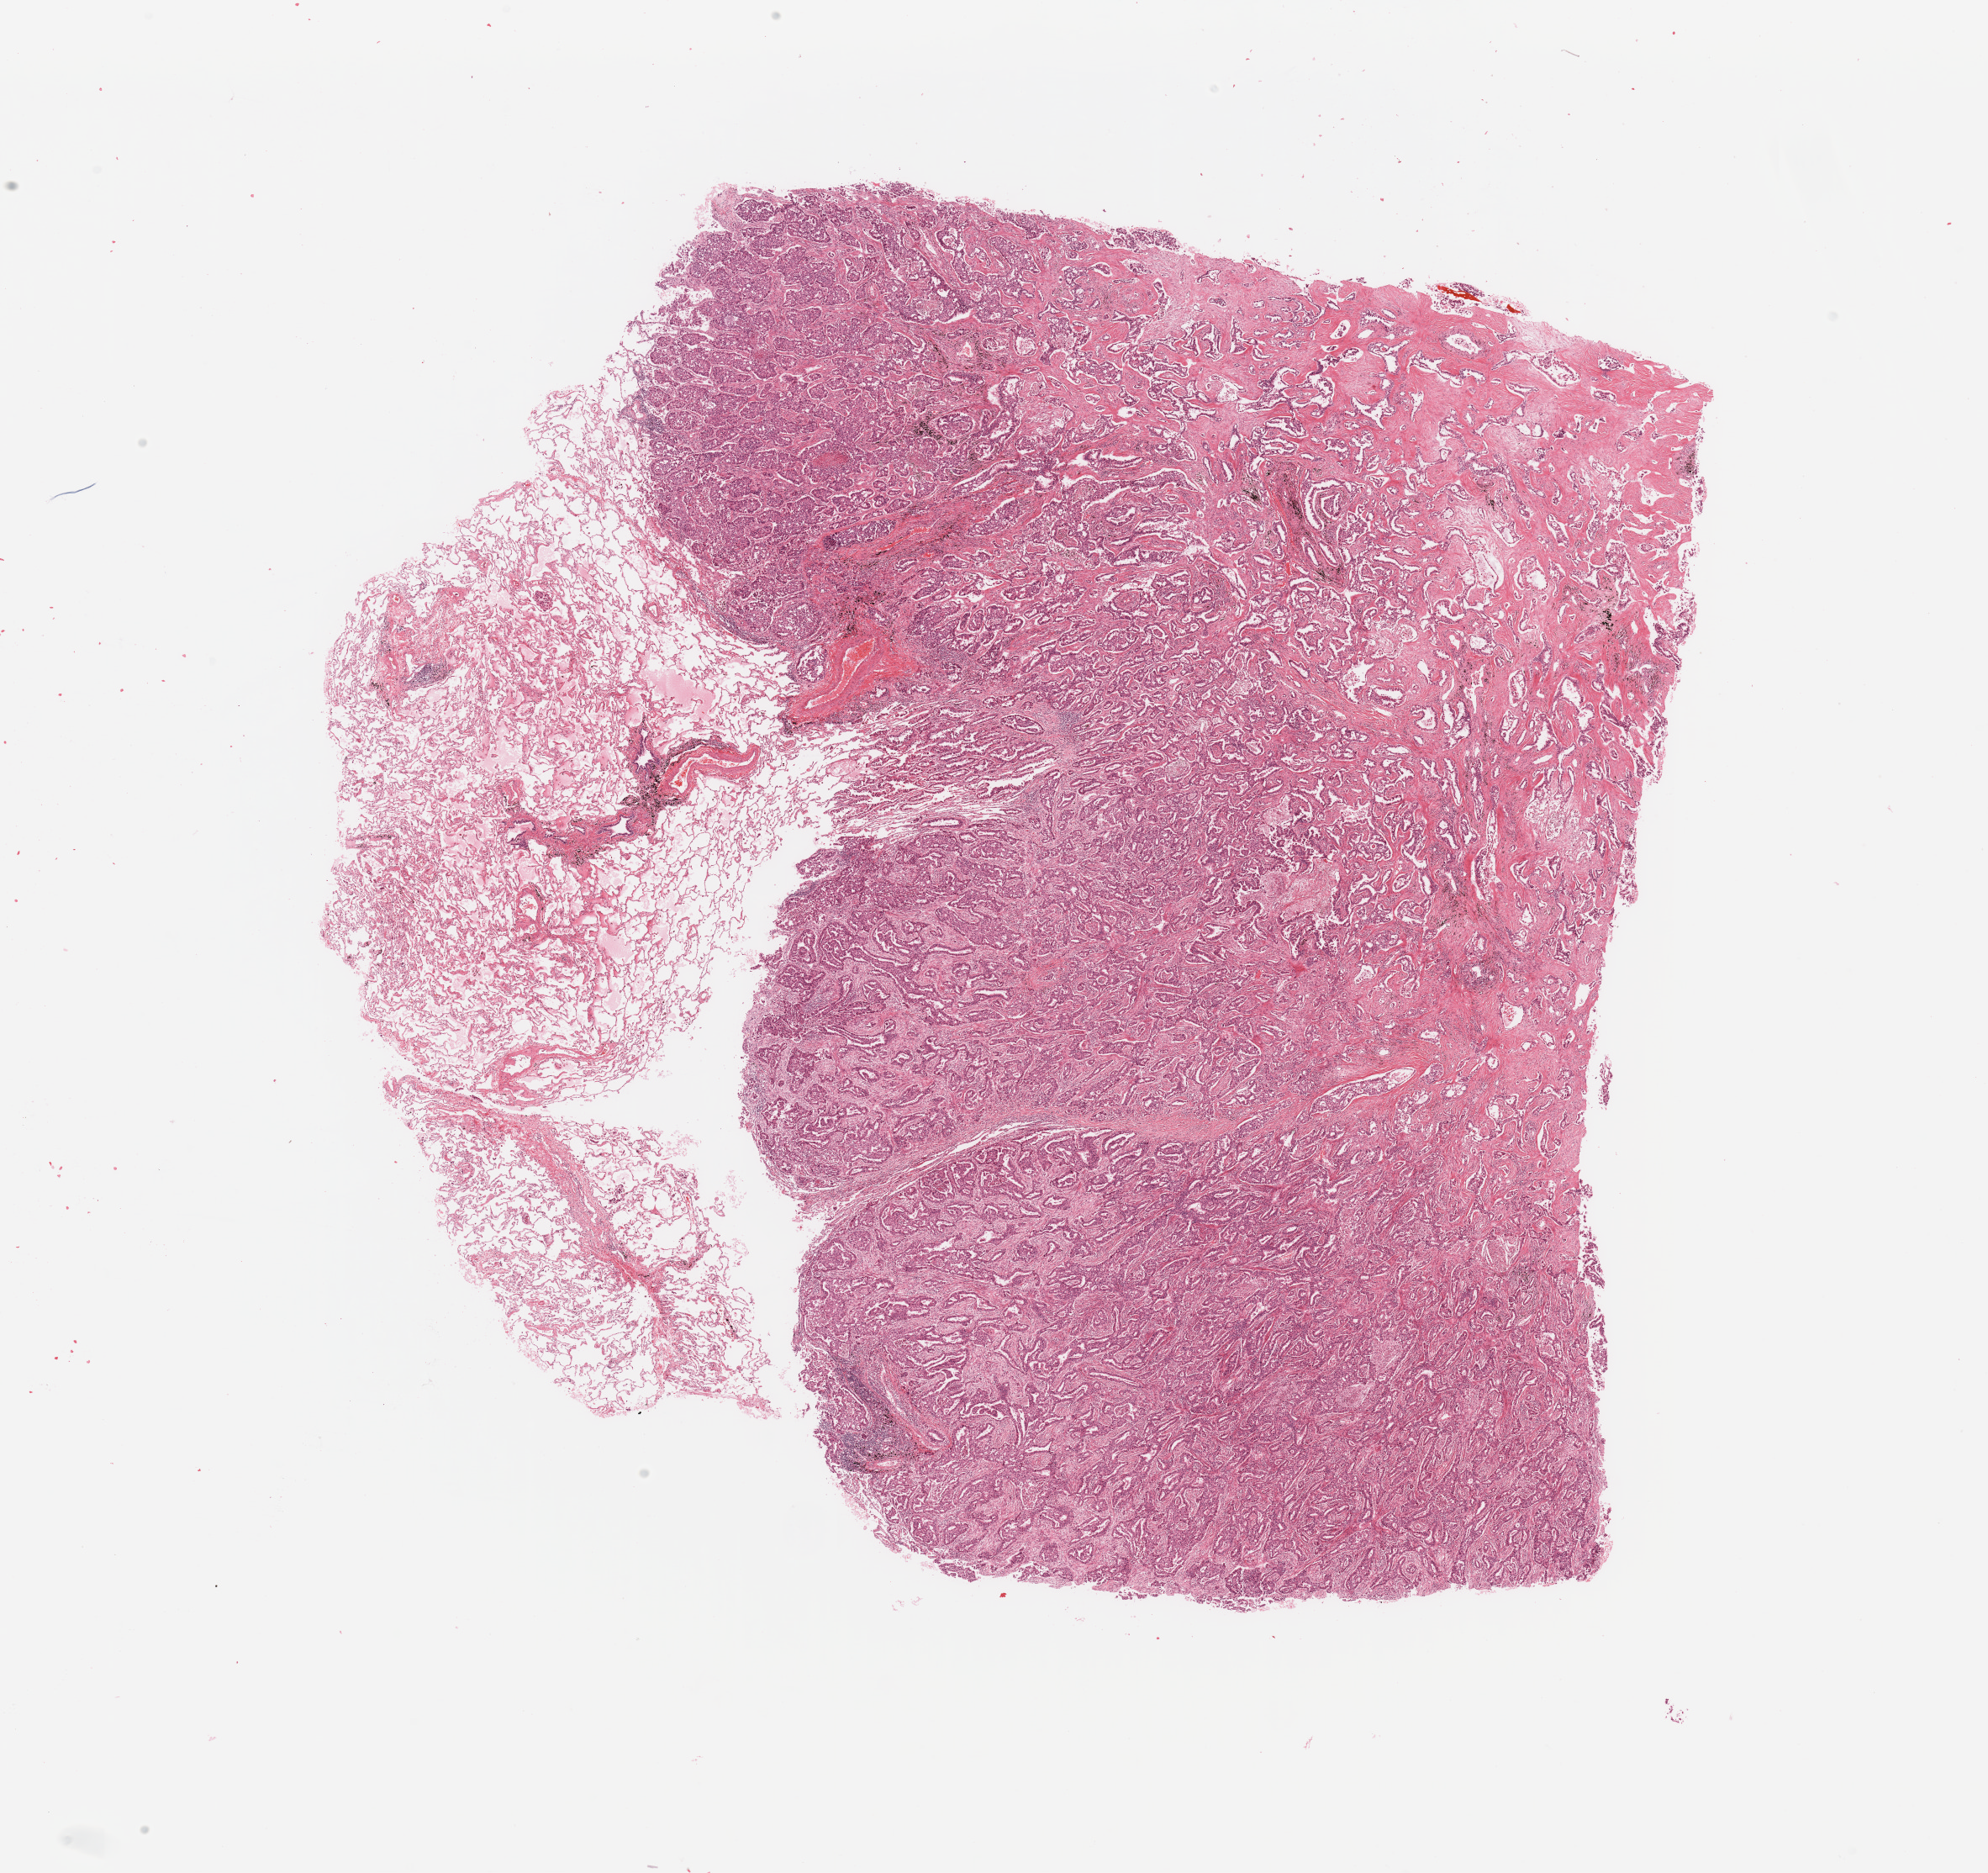
Whole-slide histology image, H&E — shown as a low-resolution overview of the whole scanned area (about 18.7 x 17.6 mm, from a 20x scan), tumour tissue sample, lung. 55-year-old female patient. Histologic grade: G2 (moderately differentiated).
* AJCC pathologic stage: IA
* diagnosis: Adenocarcinoma, NOS